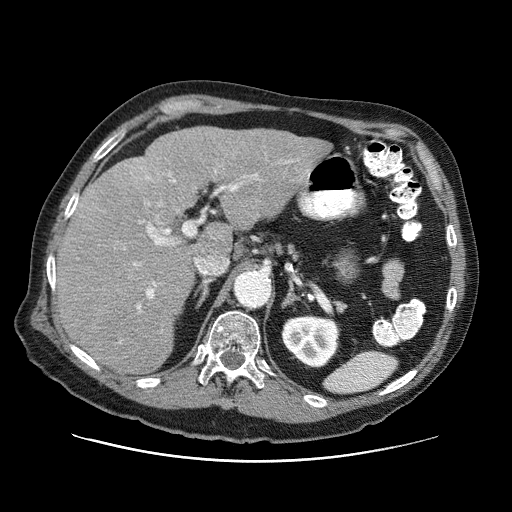
Contrast-enhanced abdominal CT (liver protocol), one axial slice; slice 45 of 87 in the series (ordered by position); reconstruction kernel STANDARD; one of 3 acquisitions stored at this slice position; soft-tissue window (W 400 / L 40 HU); 2.5 mm slice thickness; 512 × 512 image matrix. From the clinical record (not read from this slice): diagnosis: hepatocellular carcinoma (patient treated with transarterial chemoembolisation; whether this scan precedes or follows treatment is not stated here); TNM stage (as recorded): Stage-IIIA; Child-Pugh class: A; tumour differentiation: well differentiated; tumour nodularity: multinodular.
Outlined on this slice (semi-automatic segmentation, software-assisted and operator-edited):
- liver parenchyma outside the tumour (the mass and vessels are separate outlines, so this box may not span the whole liver): bounding box (x1, y1, x2, y2) in pixels: (56, 126, 330, 374)
- liver vessels: (134, 162, 288, 309)